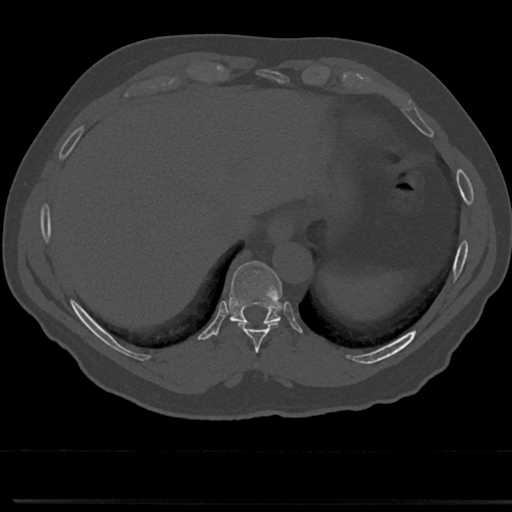
CT including the spine, one axial slice; slice 281 of 817 in the series (ordered by position); reconstruction kernel Br40s/3; 120 kVp; bone window (W 1800 / L 400 HU); 512 × 512 image matrix, field of view 355 × 355 mm. Patient: male, 61 years. From the clinical record (not read from this slice): primary cancer: prostate.
Annotated regions visible in this slice (semi-automatic segmentation, software-assisted and operator-edited):
- T10 vertebra: bounding box (x1, y1, x2, y2) in pixels: (233, 316, 278, 321)
- T8 vertebra: (254, 356, 264, 371)
- T9 vertebra: (213, 262, 302, 350)